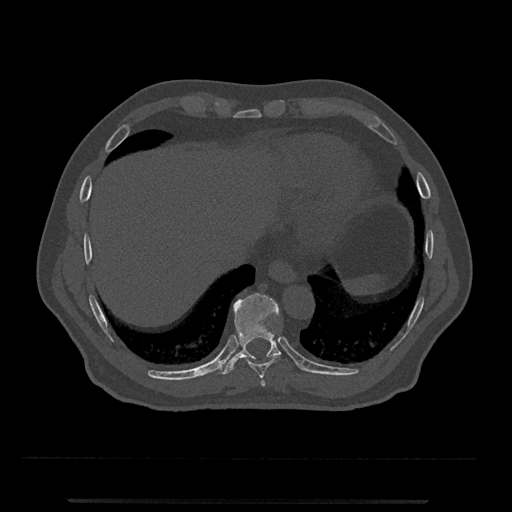
CT including the spine, one axial slice. Slice 545 of 797 in the series (ordered by position). 120 kVp. Bone window (W 1800 / L 400 HU). 0.5 mm slice thickness. 512 × 512 image matrix, field of view 419 × 419 mm. Patient: male, 63 years. From the clinical record (not read from this slice): primary cancer: prostate.
Outlined on this slice (semi-automatically segmented with operator editing):
- T10 vertebra: bounding box (x1, y1, x2, y2) in pixels: (218, 293, 281, 374)
- T8 vertebra: (260, 380, 265, 387)
- T9 vertebra: (245, 355, 281, 379)